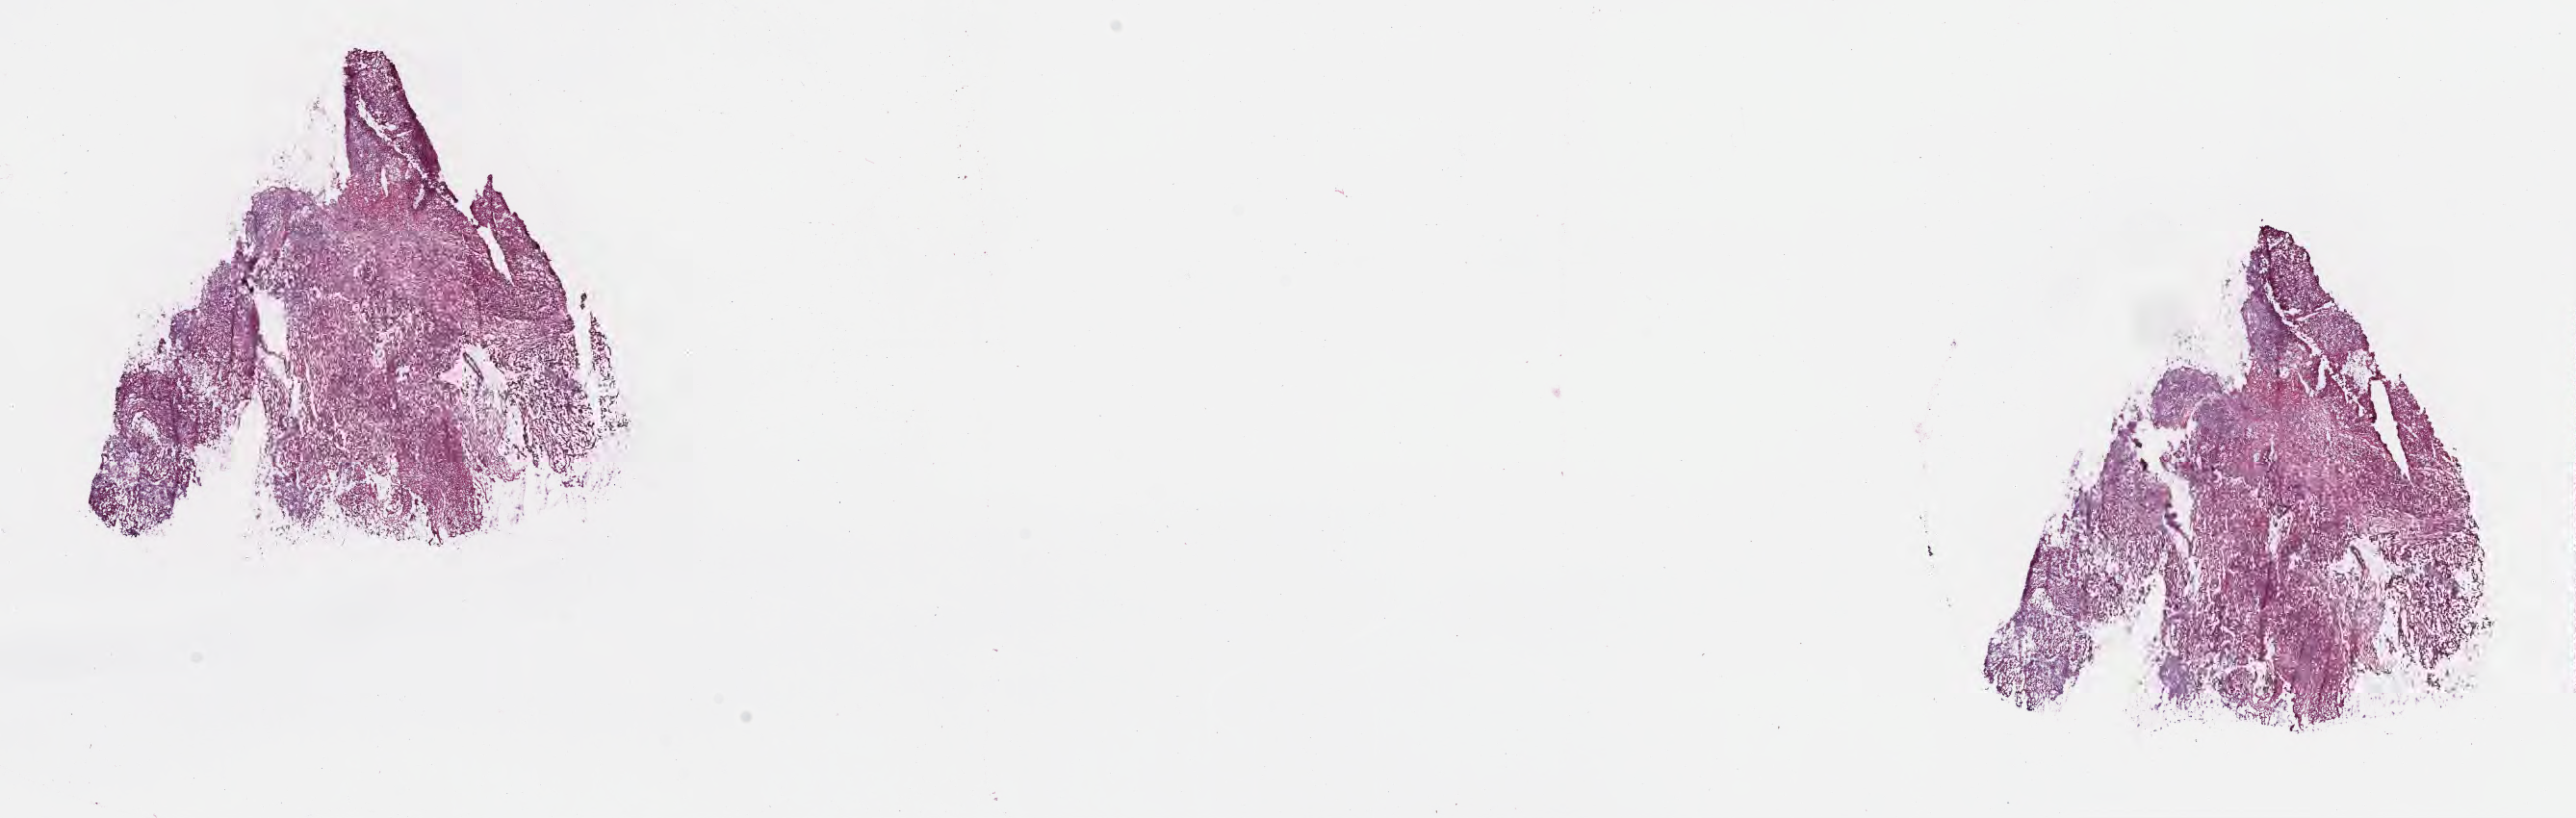
Whole-slide image, H&E stain, a low-resolution overview of the entire scanned area, about 21.6 x 6.9 mm, frozen section, specimen: metastatic tumor tissue, resected from small intestine. Male, age 58 years at initial diagnosis. Composition of this section per pathologist review: tumor cells 30%, tumor nuclei 35%, stromal cells 10%, necrosis 5%, normal cells 55%. Infiltration values recorded for this section: lymphocyte infiltration 10%, monocyte infiltration 5%, neutrophil infiltration 20%.
Section: top of the tissue portion. Patient diagnosis (primary): Malignant melanoma, NOS.